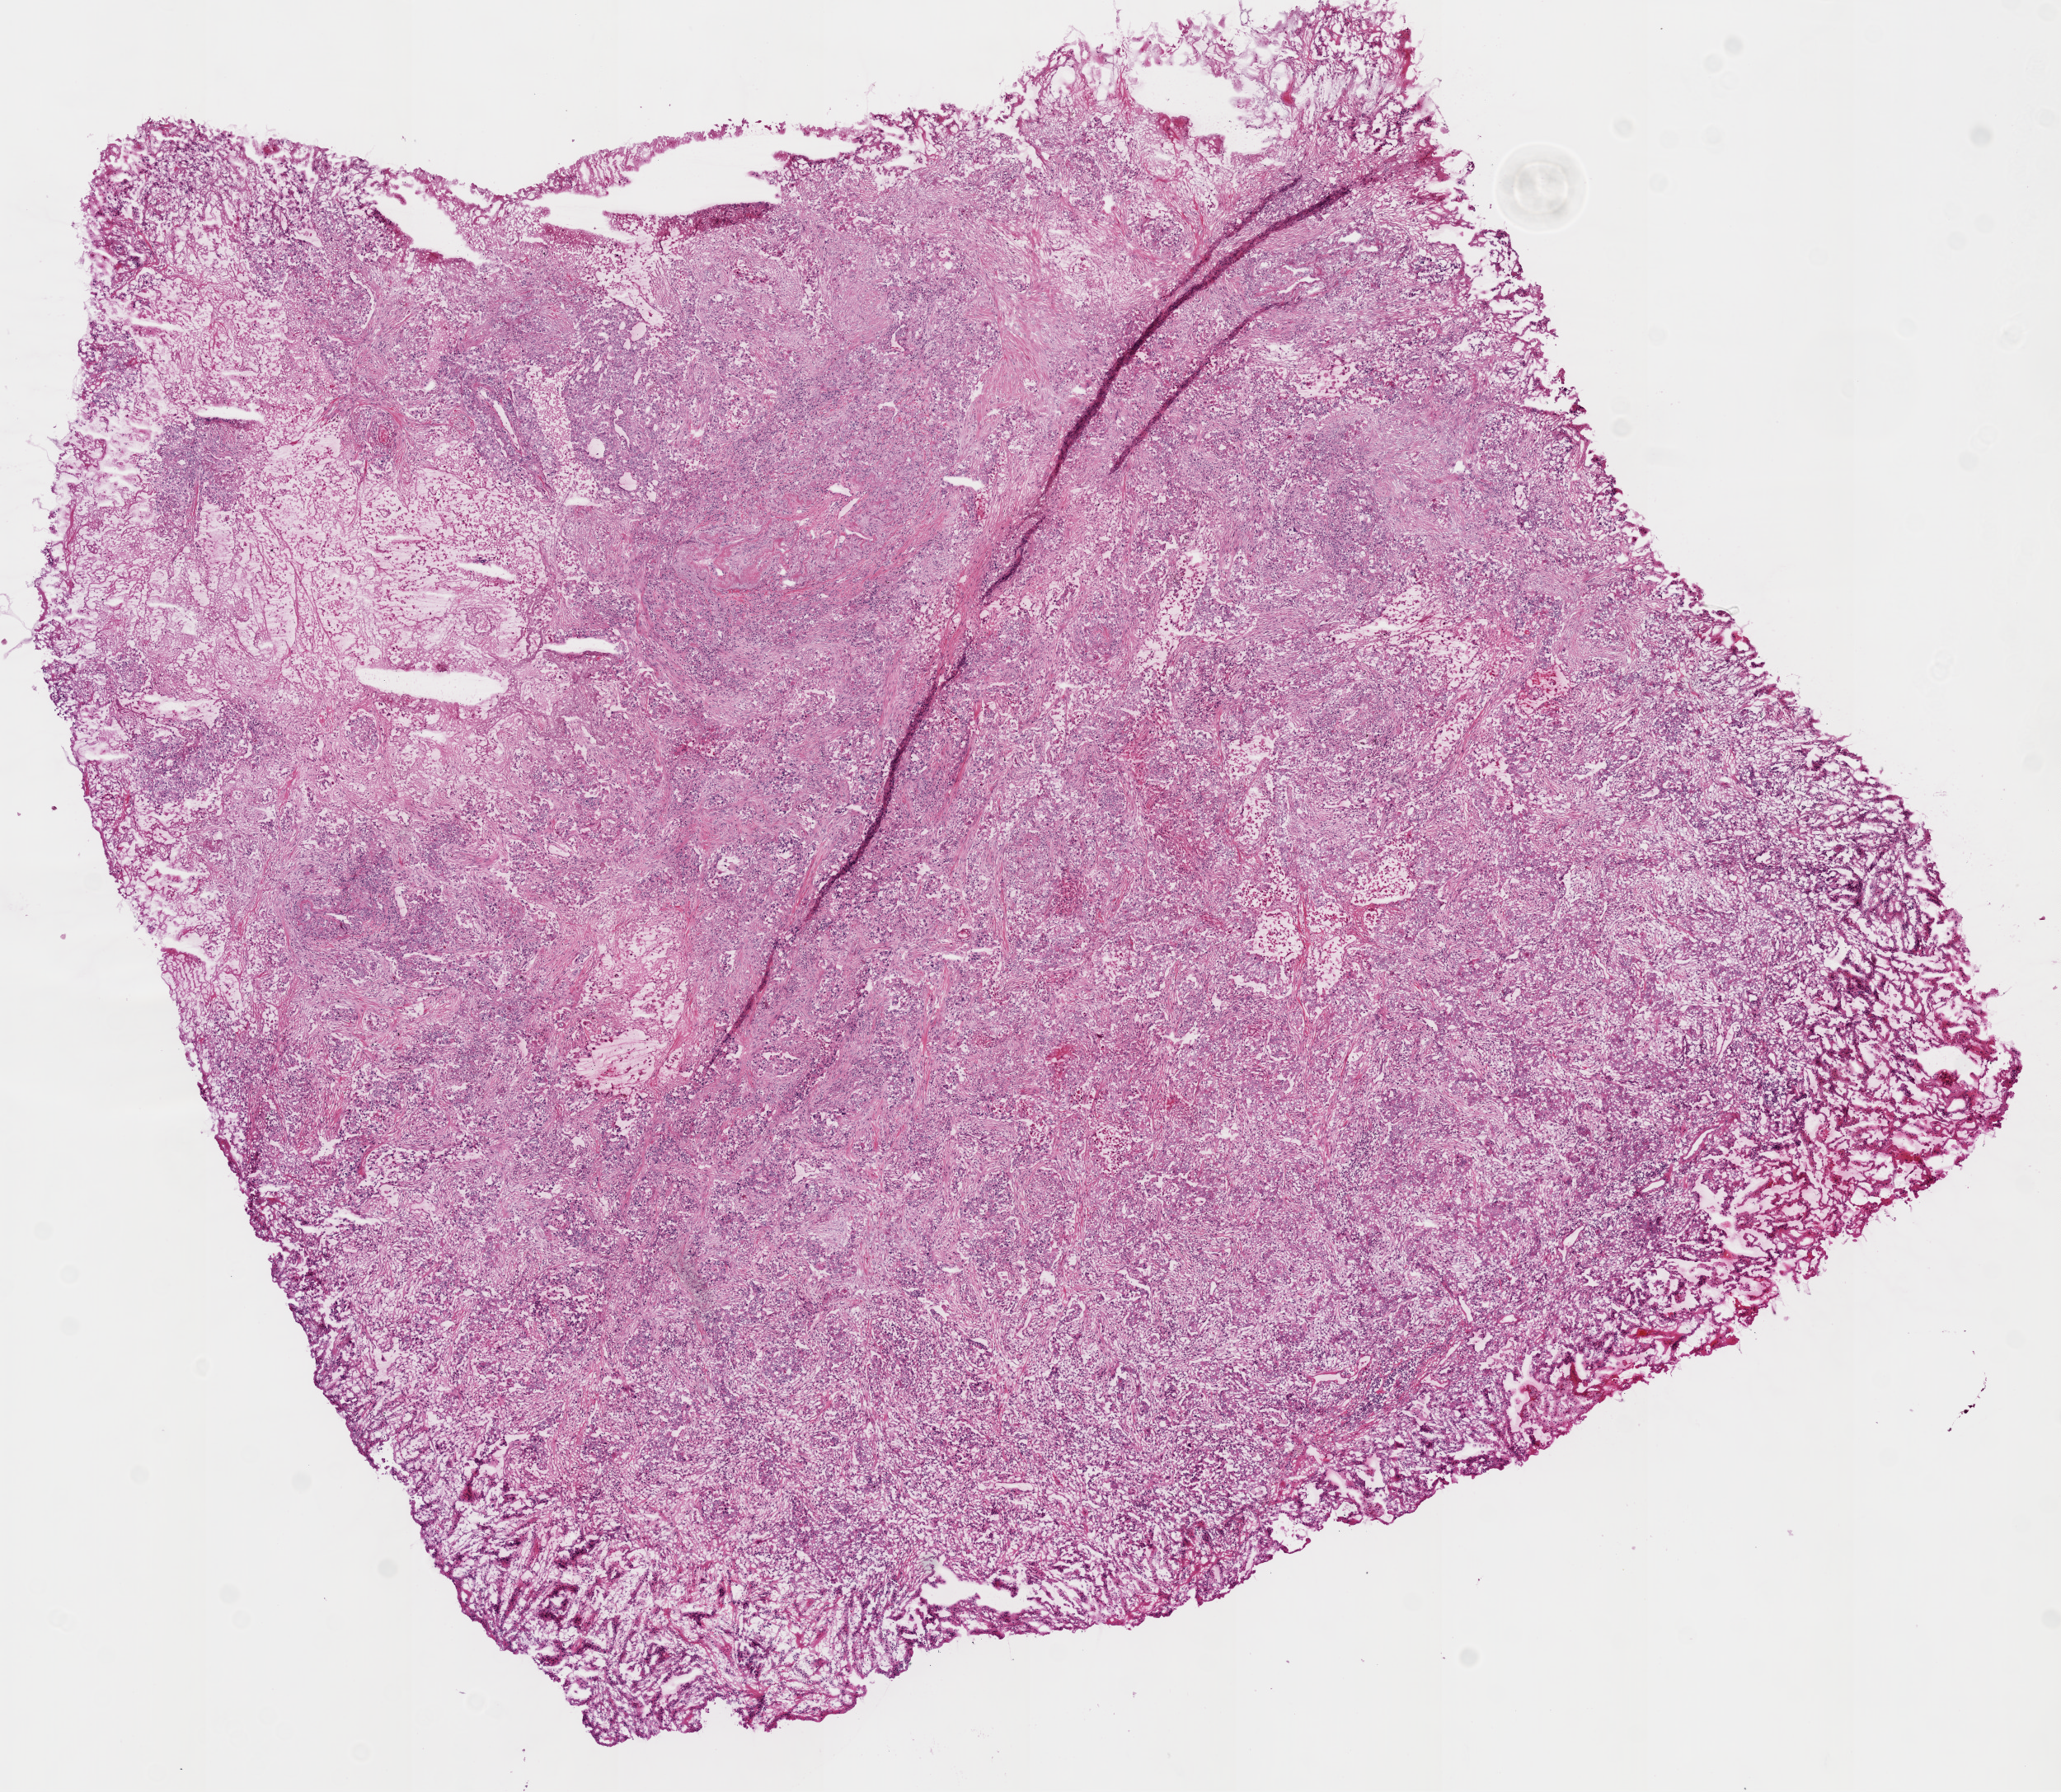
H&E whole-slide image — a low-resolution overview of the entire scanned area, about 10.0 x 8.7 mm (acquisition: 20x scan), frozen section from the top of the tissue portion, sample: primary tumour, lung. Male patient; age at initial diagnosis 74 years. Slide review estimates, as recorded: tumour cells 82%, tumour nuclei 75%, normal cells 0%, stromal cells 10%, necrosis 8%.
AJCC pathologic stage: IIB (6th edition). TNM: T2 N1 M0. Laterality: right. Histologic diagnosis: Adenocarcinoma with mixed subtypes (upper lobe, lung).